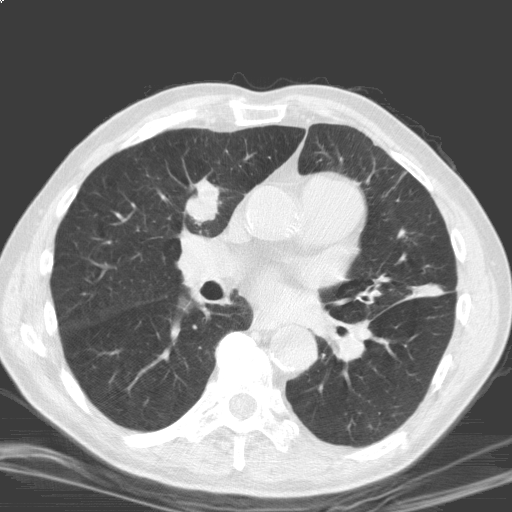
Axial slice from a low-dose chest CT screening exam, second annual screen, lung window (W 1500 / L -600 HU), standard (soft-tissue) reconstruction kernel (C), 120 kVp, slice 88 of 184 in the series, 512 × 512 image matrix, field of view 329 × 329 mm. Male, age 69 years at enrolment. Current smoker at enrolment.
Lesion marked by an expert reader, bounding box [x1, y1, x2, y2] px = [172, 171, 232, 228]. The screening reader recorded 2 non-calcified nodules or masses ≥4 mm on this exam; which of them this box marks is not recorded. Official screen result: positive, other. Later outcome: lung cancer diagnosed 17 days after this screen — squamous cell carcinoma, NOS, right upper lobe, moderately differentiated (G2), stage IB (AJCC 6th edition), 40 mm at pathology.